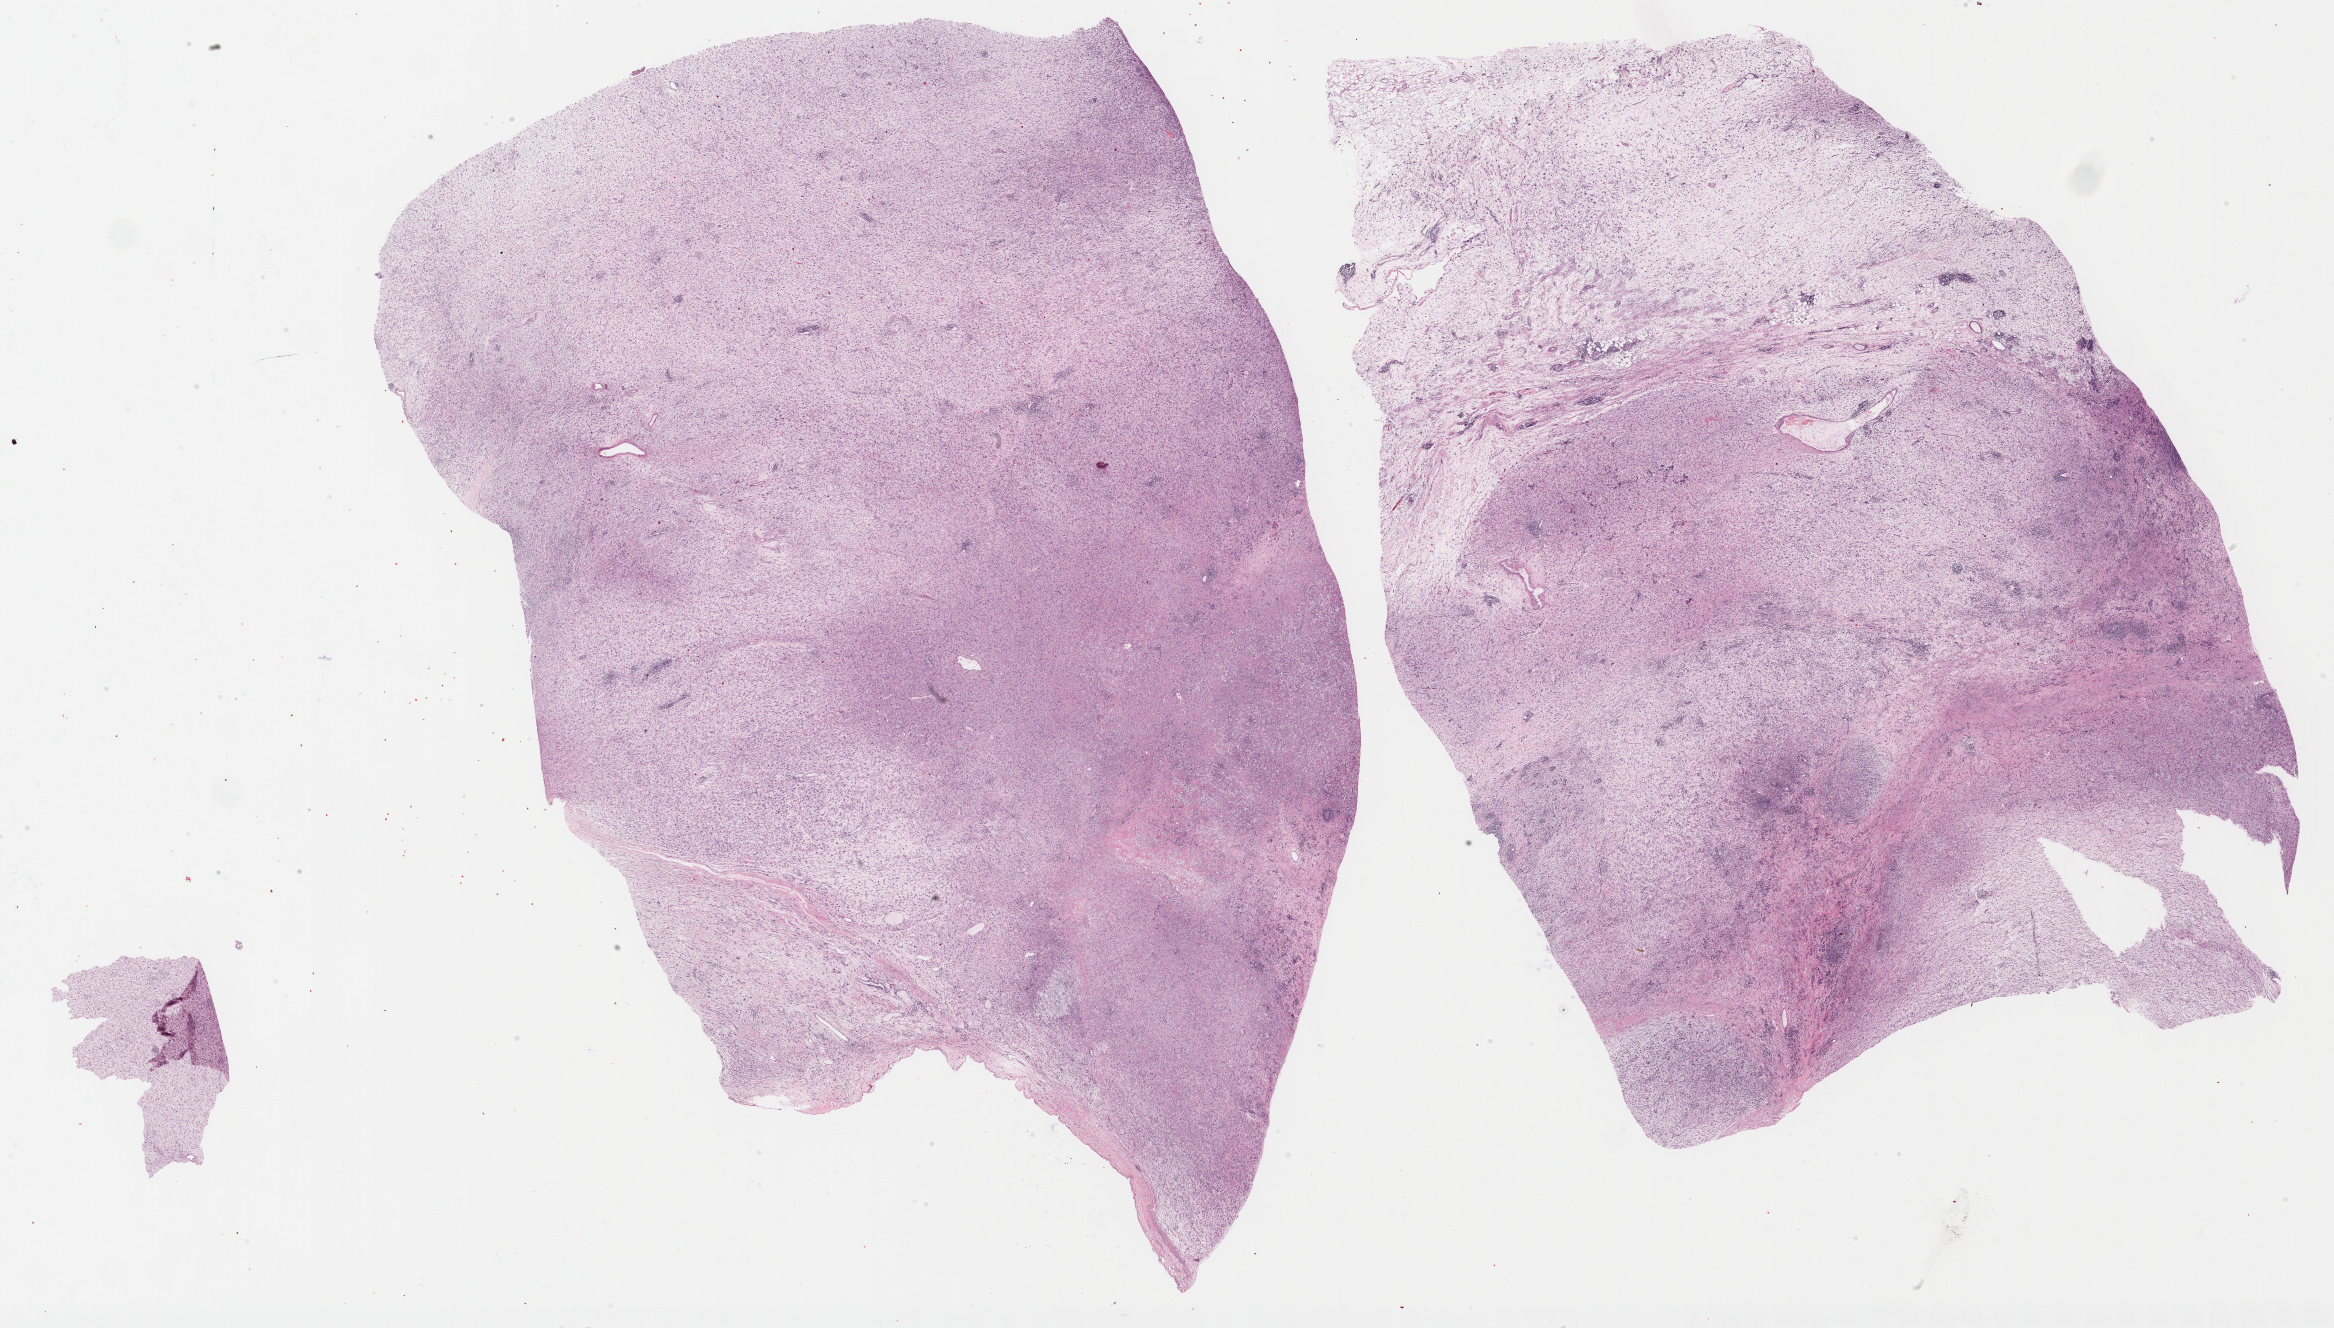
Digitized H&E tissue section (whole slide) — low-resolution overview of the scanned area, about 37.8 x 21.5 mm. FFPE section. Retroperitoneum and peritoneum, primary tumour sample. Patient: male, age at initial diagnosis 59 years.
Pathologic diagnosis: Dedifferentiated liposarcoma (retroperitoneum).